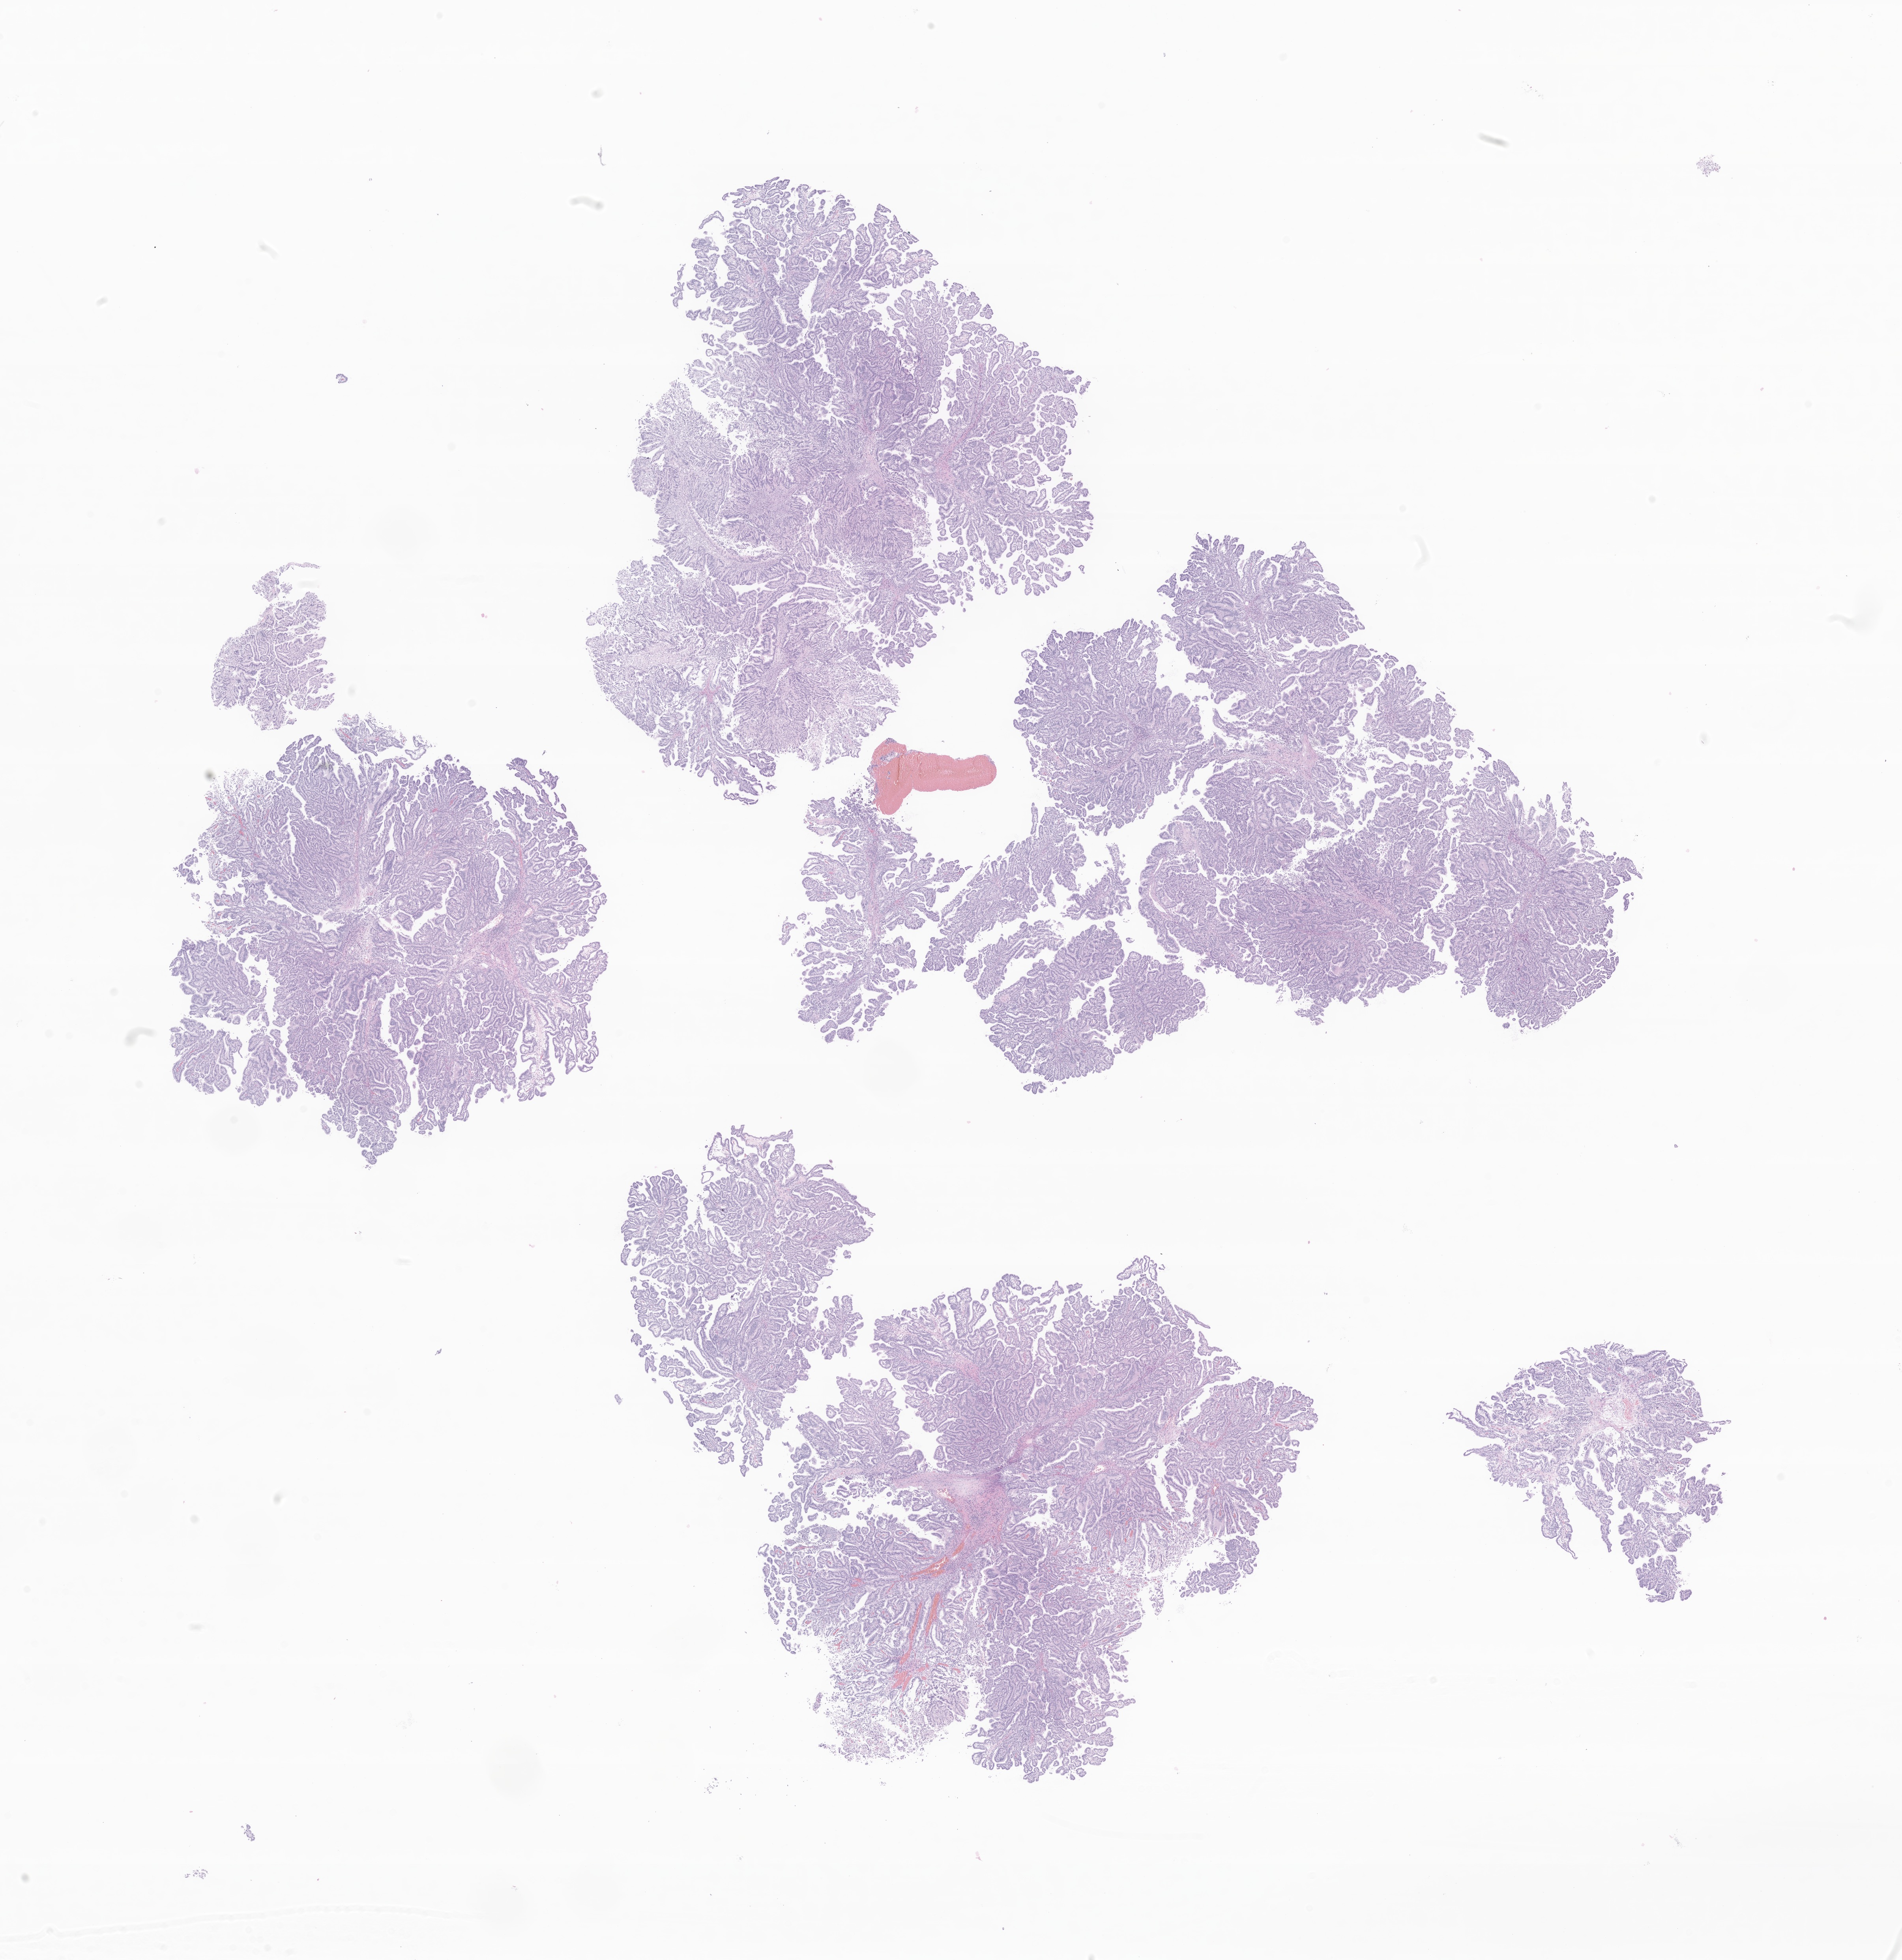
Whole-slide image, haematoxylin and eosin stain of tumor tissue from the cerebral ventricle — a low-resolution overview of the entire scanned area, about 20.3 x 20.9 mm, formalin-fixed paraffin-embedded section. Patient: female, age 40 months.
Diagnosis (ICD-O-3 morphology term): Choroid plexus papilloma, NOS.